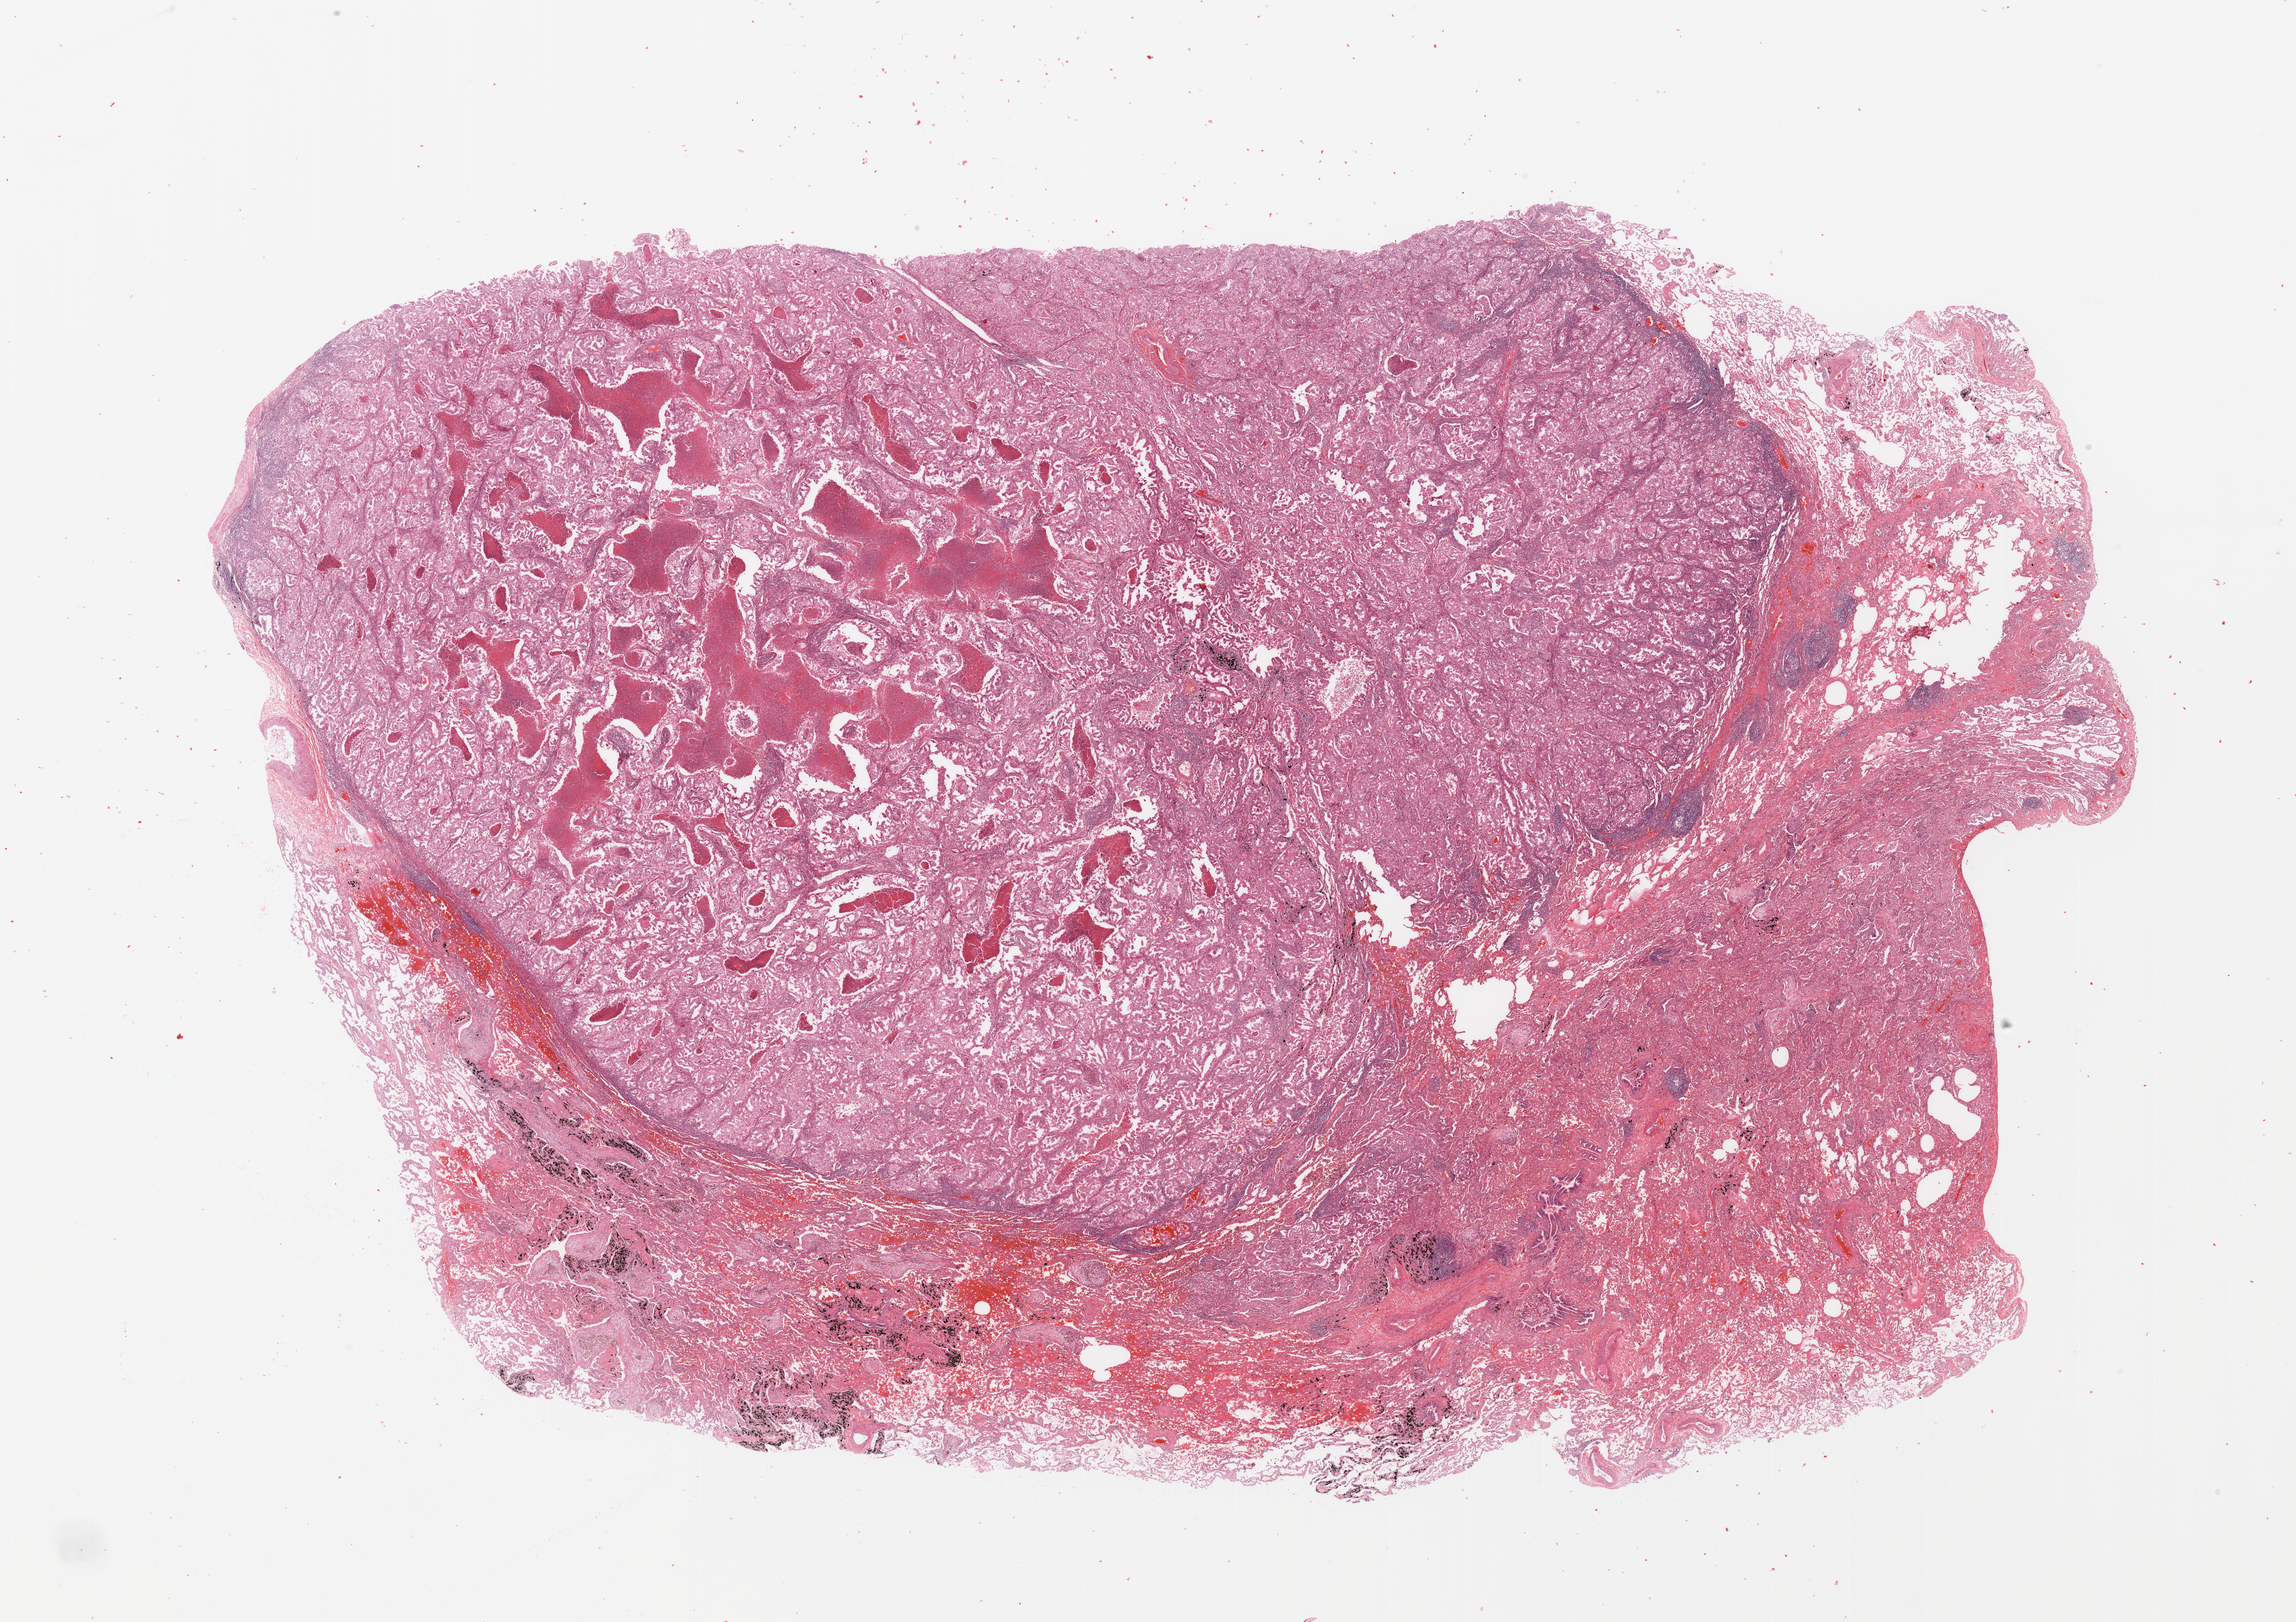
H&E whole-slide image, shown as a low-resolution overview of the whole scanned area (about 29.5 x 20.9 mm); tumour tissue sample, lung. Patient: male, age 56 years. Histologic grade: G3 (poorly differentiated).
AJCC pathologic stage: IB. Diagnosis: Adenocarcinoma, NOS.